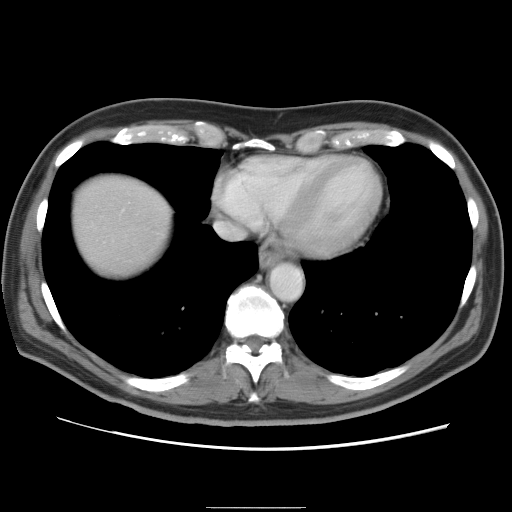
Contrast-enhanced abdominal CT, one axial slice; position 79 of 87 along the scan axis; 120 kVp; soft-tissue window (W 400 / L 40 HU); 5 mm slice thickness; 512 × 512 image matrix, field of view 363 × 363 mm. Male patient, age 63 years. From the clinical record (not read from this slice): diagnosis: colorectal cancer liver metastases, imaged before liver resection; multiple liver metastases: no; largest metastasis: 9 cm; chemotherapy before resection: no.
Annotated regions visible in this slice (manually delineated by an expert):
- liver: bounding box (x1, y1, x2, y2) in pixels: (74, 176, 172, 272)
- planned liver remnant (the part of the liver to remain after resection): (74, 186, 172, 272)